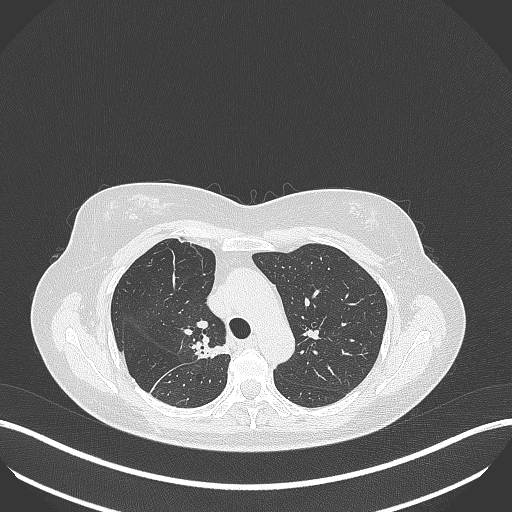
Chest CT, one axial slice; position 277 of 386 along the scan axis; lung window (W 1500 / L -600 HU); 512 × 512 image matrix. Female patient, age 65 years. Case-level facts recorded for this patient, not image findings: clinical TNM (as recorded): T1b N0 M0; histopathological grade: G2.
Structures marked on this image (rectangle marked by the reading radiologist):
- lung tumour (recorded histology: adenocarcinoma): bounding box <190,336,232,367> (left, top, right, bottom; pixels)